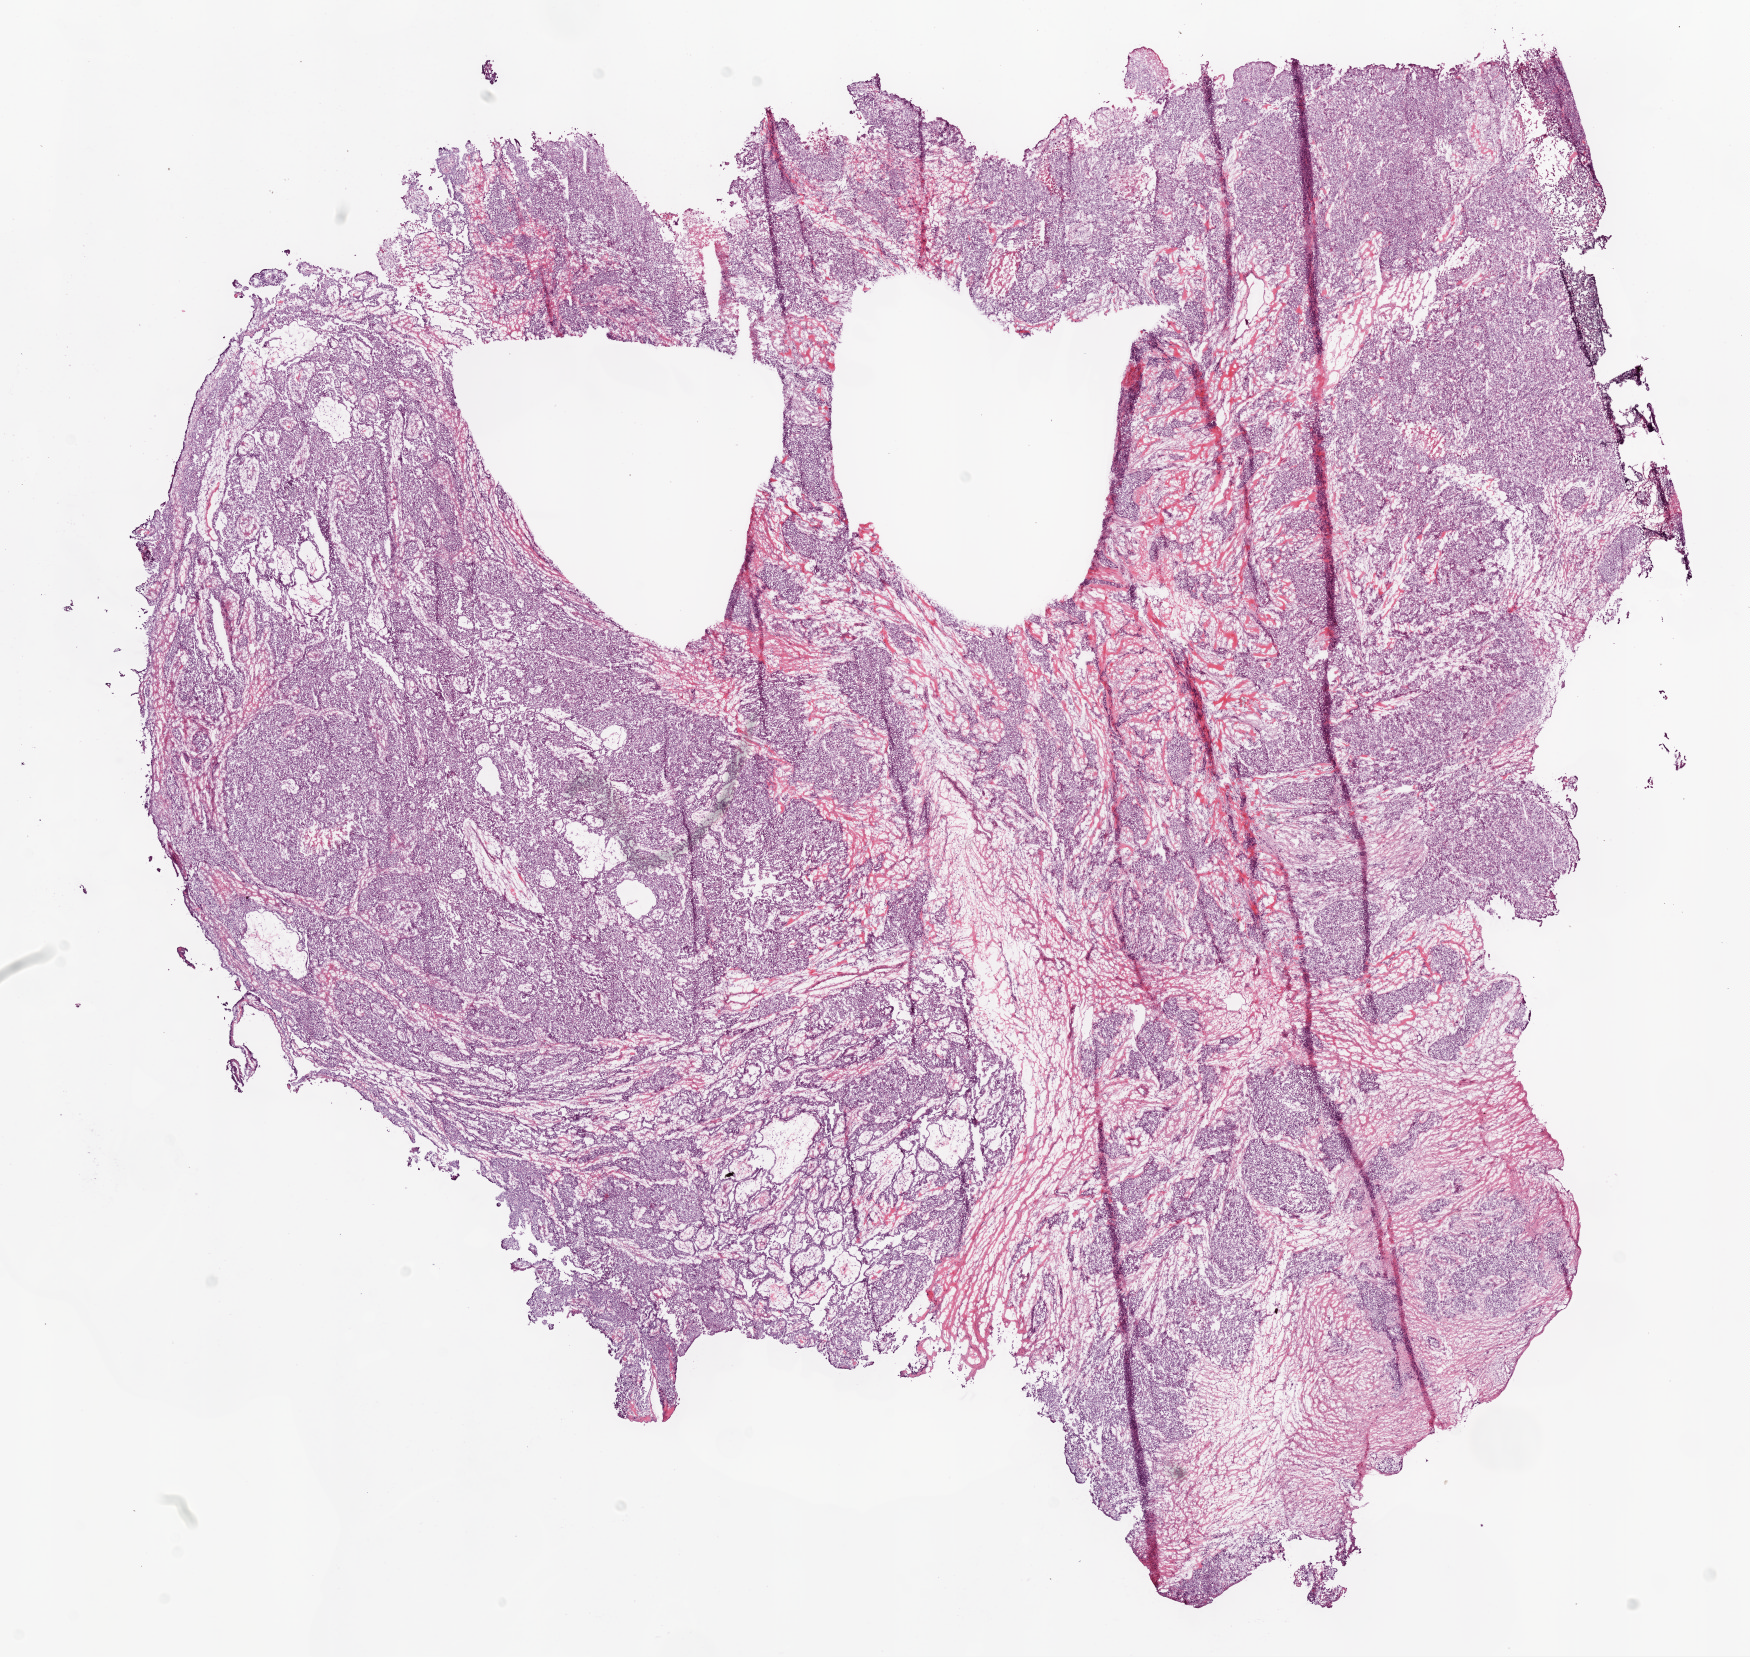
Whole-slide histology image, Hematoxylin and eosin (H&E) stained — a low-resolution overview of the entire scanned area, about 14.0 x 13.3 mm. Frozen section. Sample: primary tumour, ovary. Female, age 58 years at initial diagnosis. Histologic grade: G3 (poorly differentiated). Pathologist review of this section (percent, as recorded): tumour cells 85%, tumour nuclei 90%, normal cells 0%, stromal cells 15%, necrosis 0%. Infiltration values recorded for this section: lymphocyte infiltration 5%.
• FIGO stage: IIIC
• diagnosis: Serous cystadenocarcinoma, NOS
• laterality: right